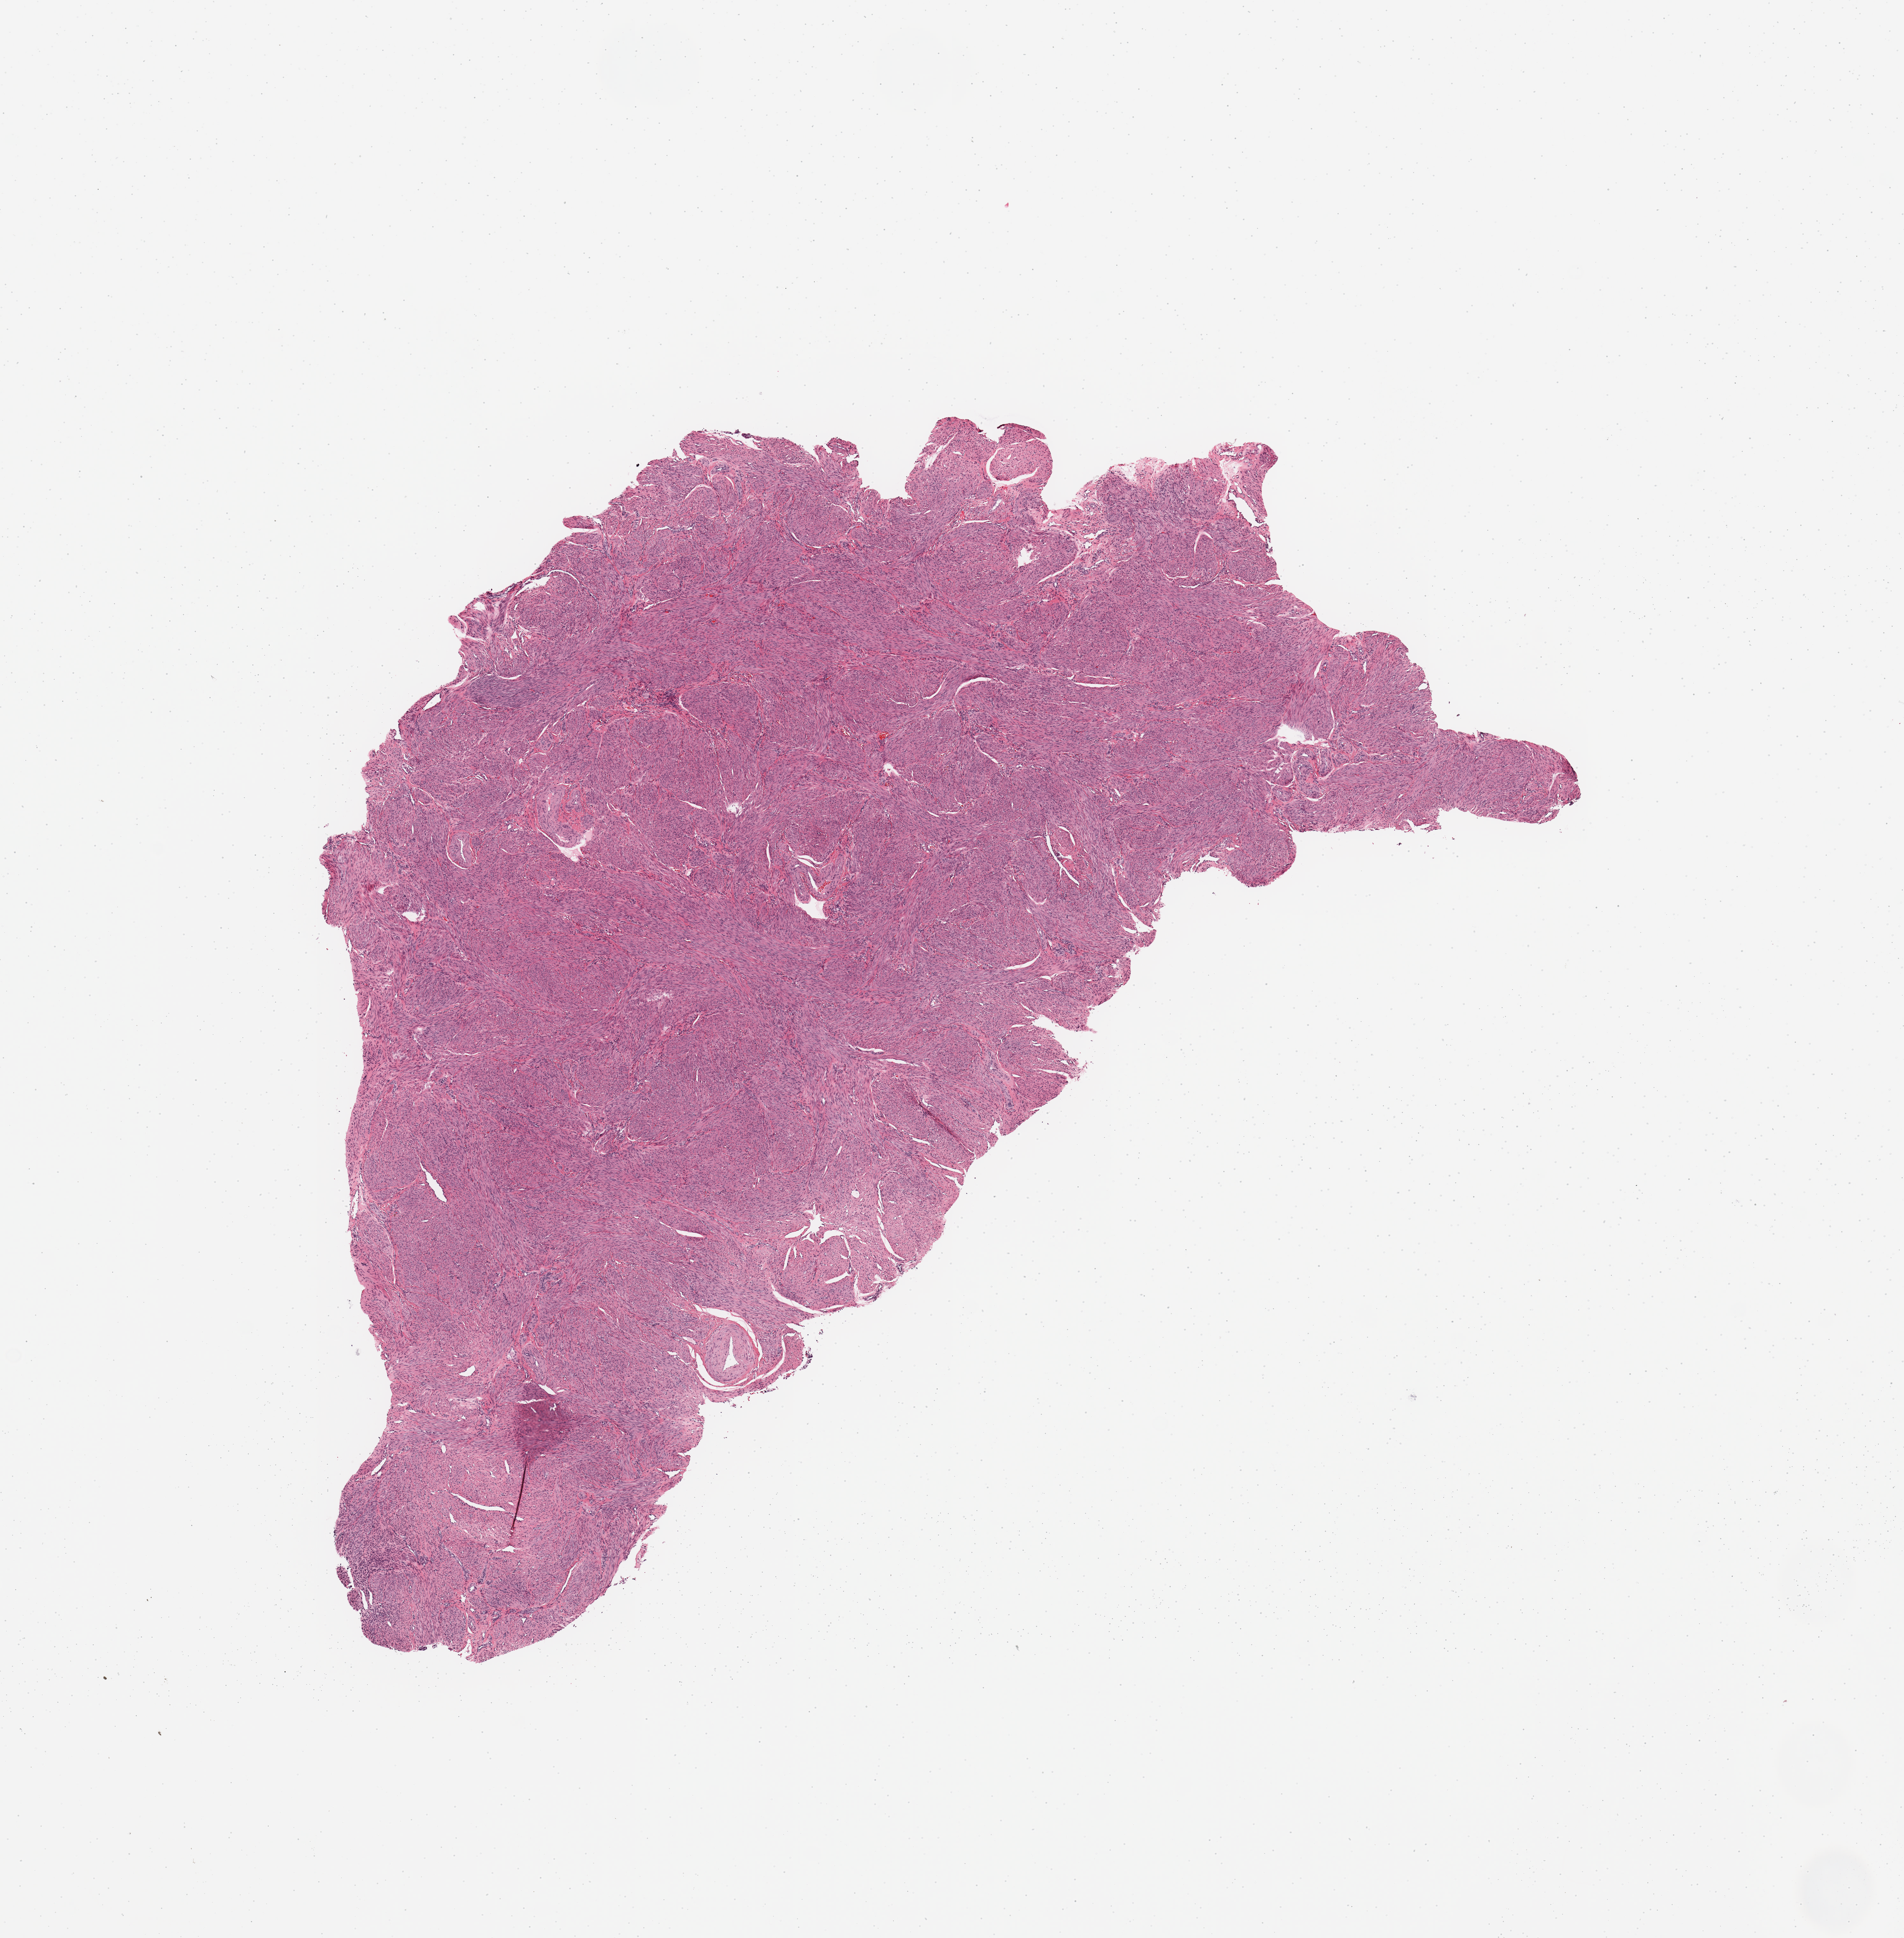
H&E-stained whole-slide image, low-resolution overview of the scanned area, about 11.8 x 12.0 mm; uterus, normal (non-tumour) tissue. Female, 56 y/o.
This section: normal (non-tumour) tissue from the same patient. Patient diagnosis: Endometrioid adenocarcinoma, NOS.